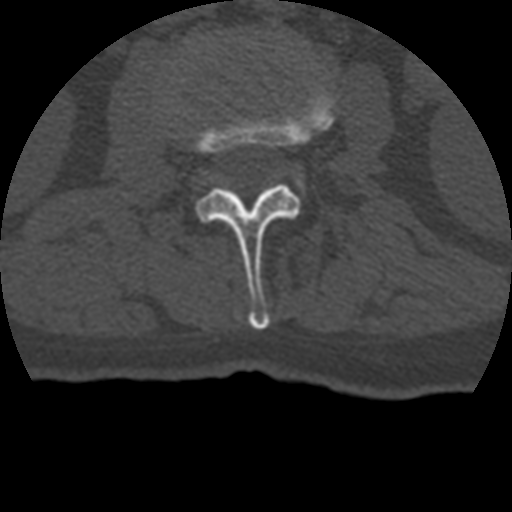
CT including the spine, one axial slice. Slice 109 of 399 in the series (ordered by position). Reconstruction kernel STANDARD. 120 kVp. Bone window (W 1800 / L 400 HU). 512 × 512 image matrix. Patient age 69 years. Case-level facts recorded for this patient, not image findings: primary cancer: prostate.
Annotated regions visible in this slice (semi-automatic segmentation, software-assisted and operator-edited):
- L2 vertebra: bounding box <194,86,334,329> (left, top, right, bottom; pixels)